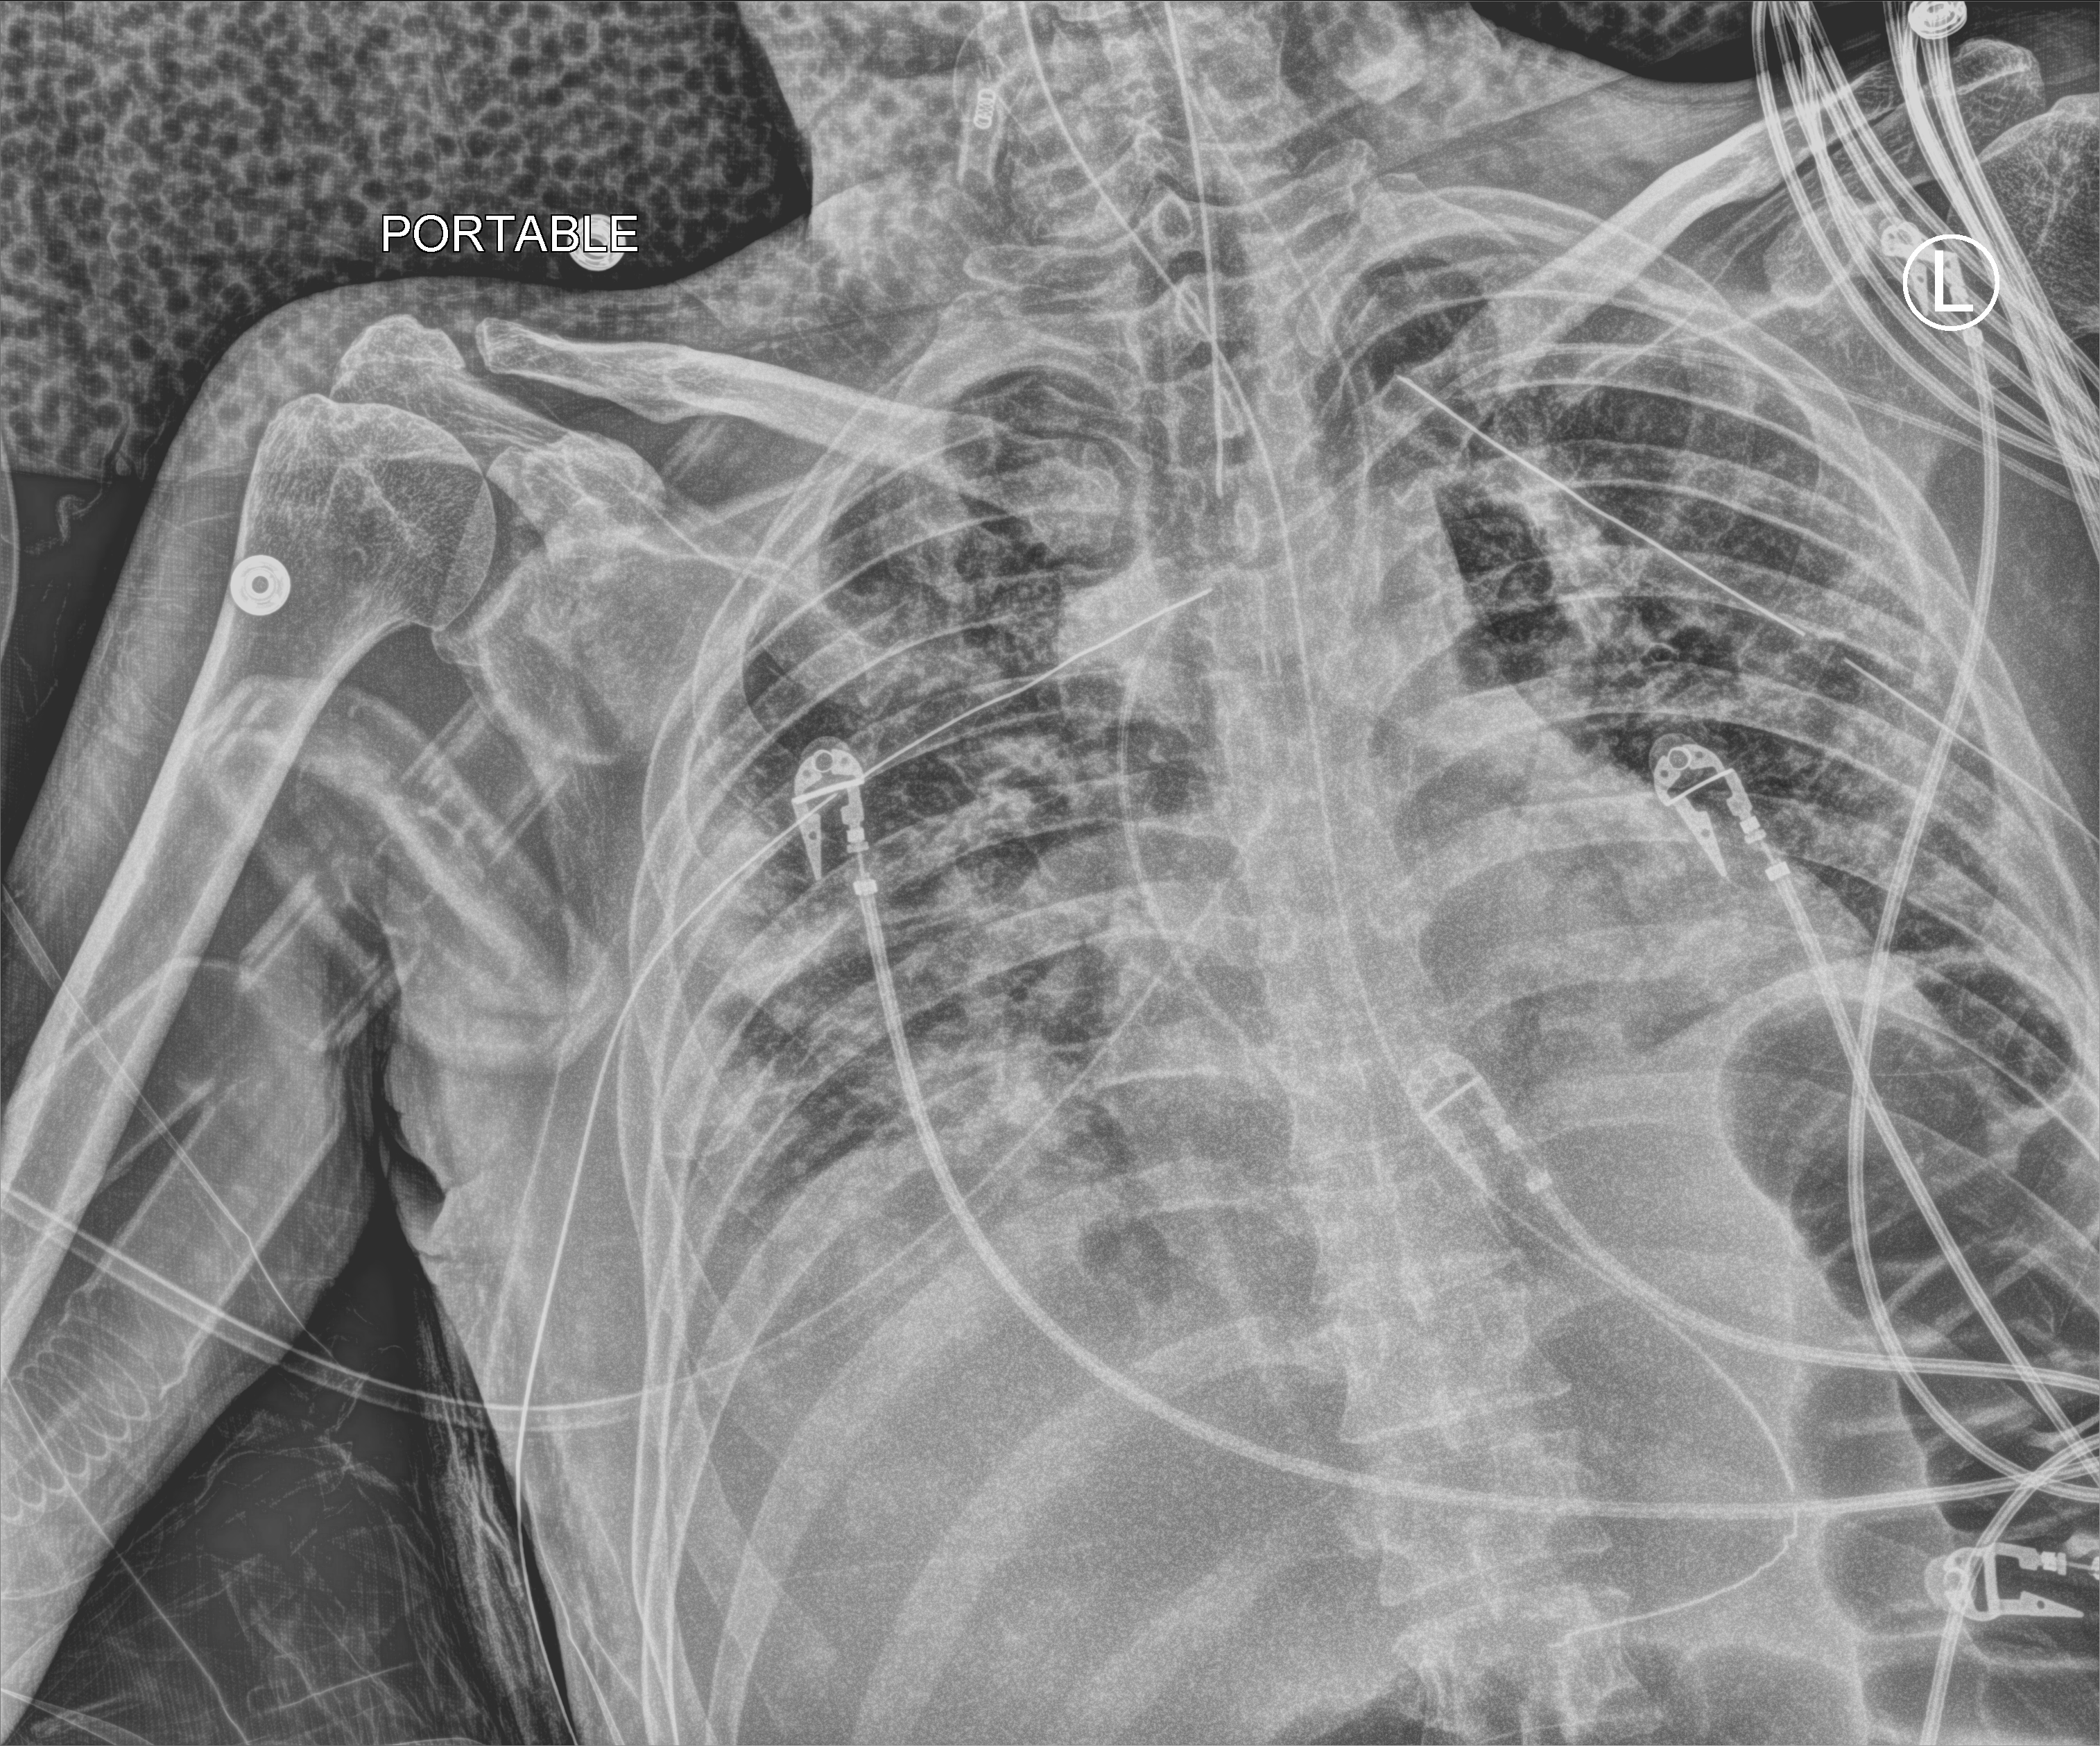
Chest X-ray (portable), anteroposterior (AP) projection. Male patient hospitalised with COVID-19, age 18–59 years.
From the hospital-stay record, not from the radiograph (when in the stay this image was taken is not recorded): COPD (admission record): no.